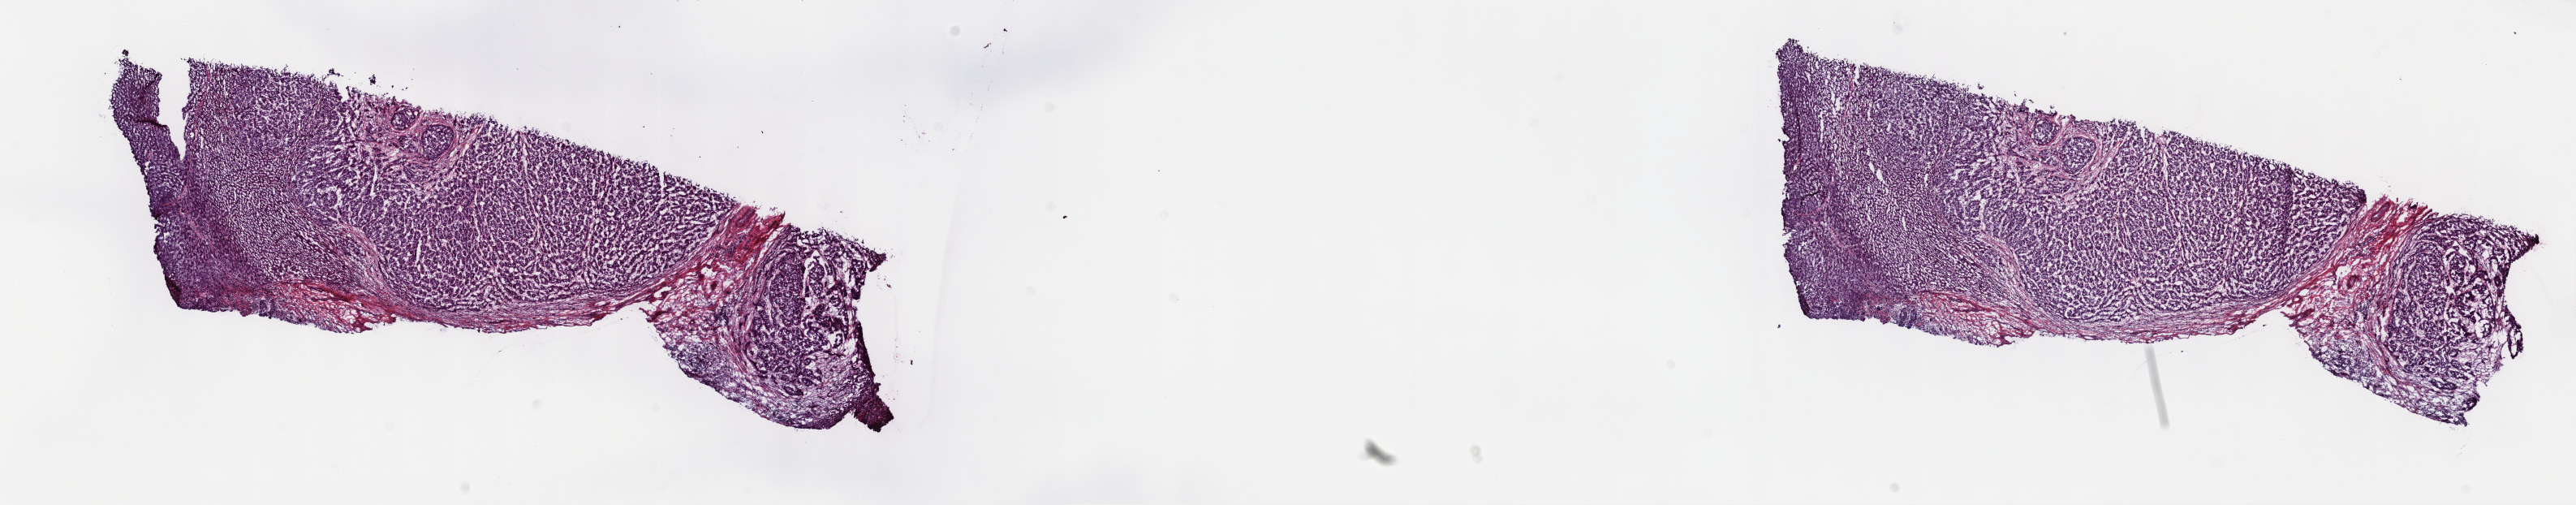
Digitized H&E tissue section (whole slide) — low-resolution overview of the scanned area, about 25.7 x 5.0 mm (slide scanned at 40x); frozen section from the top of the tissue portion; sample: primary tumour, liver. Patient: male, age at initial diagnosis 48 years. Histologic grade: G3 (poorly differentiated). Composition of this section per pathologist review: tumour cells 60%, tumour nuclei 60%, normal cells 25%, stromal cells 15%, necrosis 0%. Inflammatory infiltration, as recorded: lymphocyte infiltration 3%, monocyte infiltration 1%, neutrophil infiltration 2%.
AJCC pathologic stage: II (6th edition). Histologic diagnosis: Hepatocellular carcinoma, NOS.